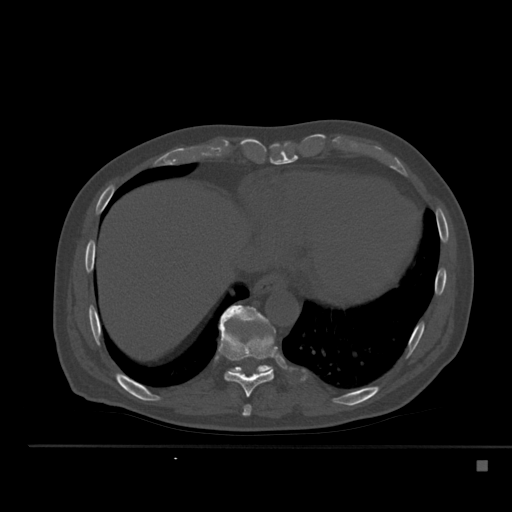
CT including the spine, one axial slice. Position 284 of 517 along the scan axis. 120 kVp. Bone window (W 1800 / L 400 HU). 512 × 512 image matrix, field of view 408 × 408 mm. Male patient, age 70 years. From the clinical record (not read from this slice): primary cancer: renal.
Annotated regions visible in this slice (semi-automatic segmentation, software-assisted and operator-edited):
- T10 vertebra: bounding box [x1, y1, x2, y2] px = [221, 305, 273, 374]
- T8 vertebra: [242, 405, 251, 416]
- T9 vertebra: [218, 318, 277, 397]